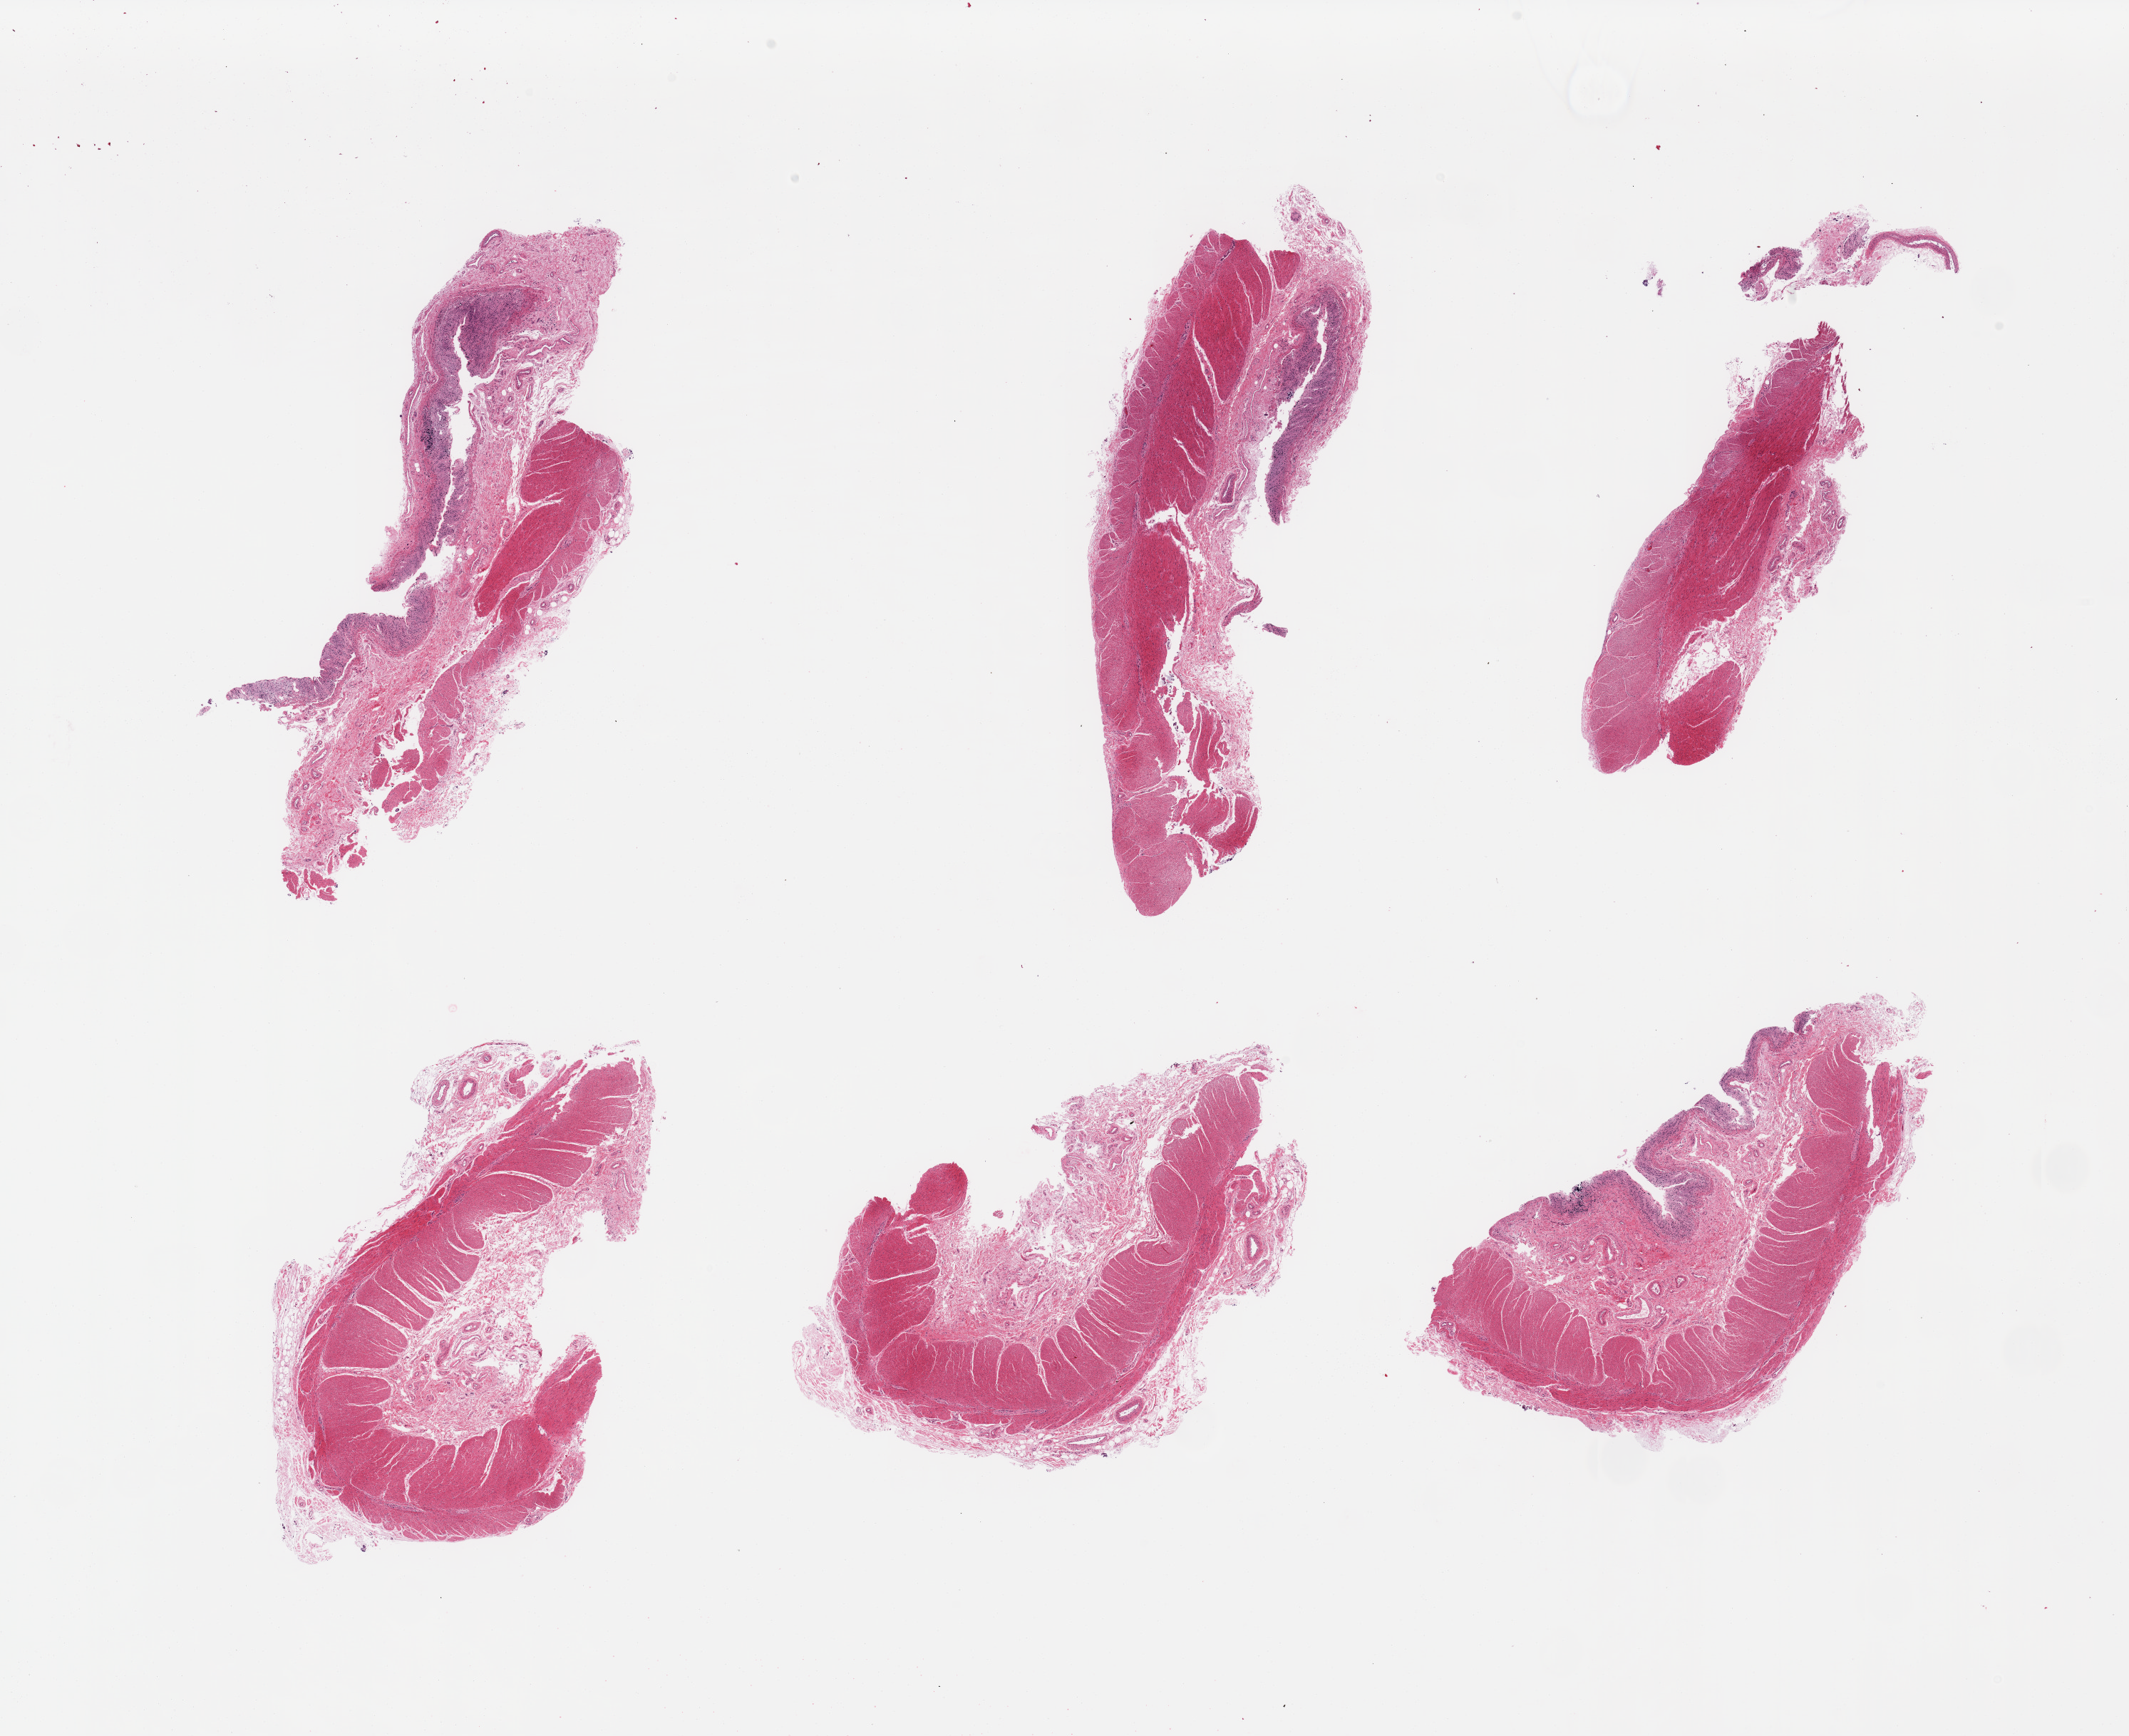
H&E whole-slide image, a low-resolution overview of the entire scanned area, about 23.6 x 19.3 mm (acquisition: 20x scan). PAXgene-fixed, paraffin-embedded tissue. Target tissue: sigmoid colon. Tissue donor sample. Male donor.
* reviewer comment on this tissue sample: 6 pieces, ~60% target muscularis; rest is adherent sersoal fat/connective tissue elements, focal mucosa